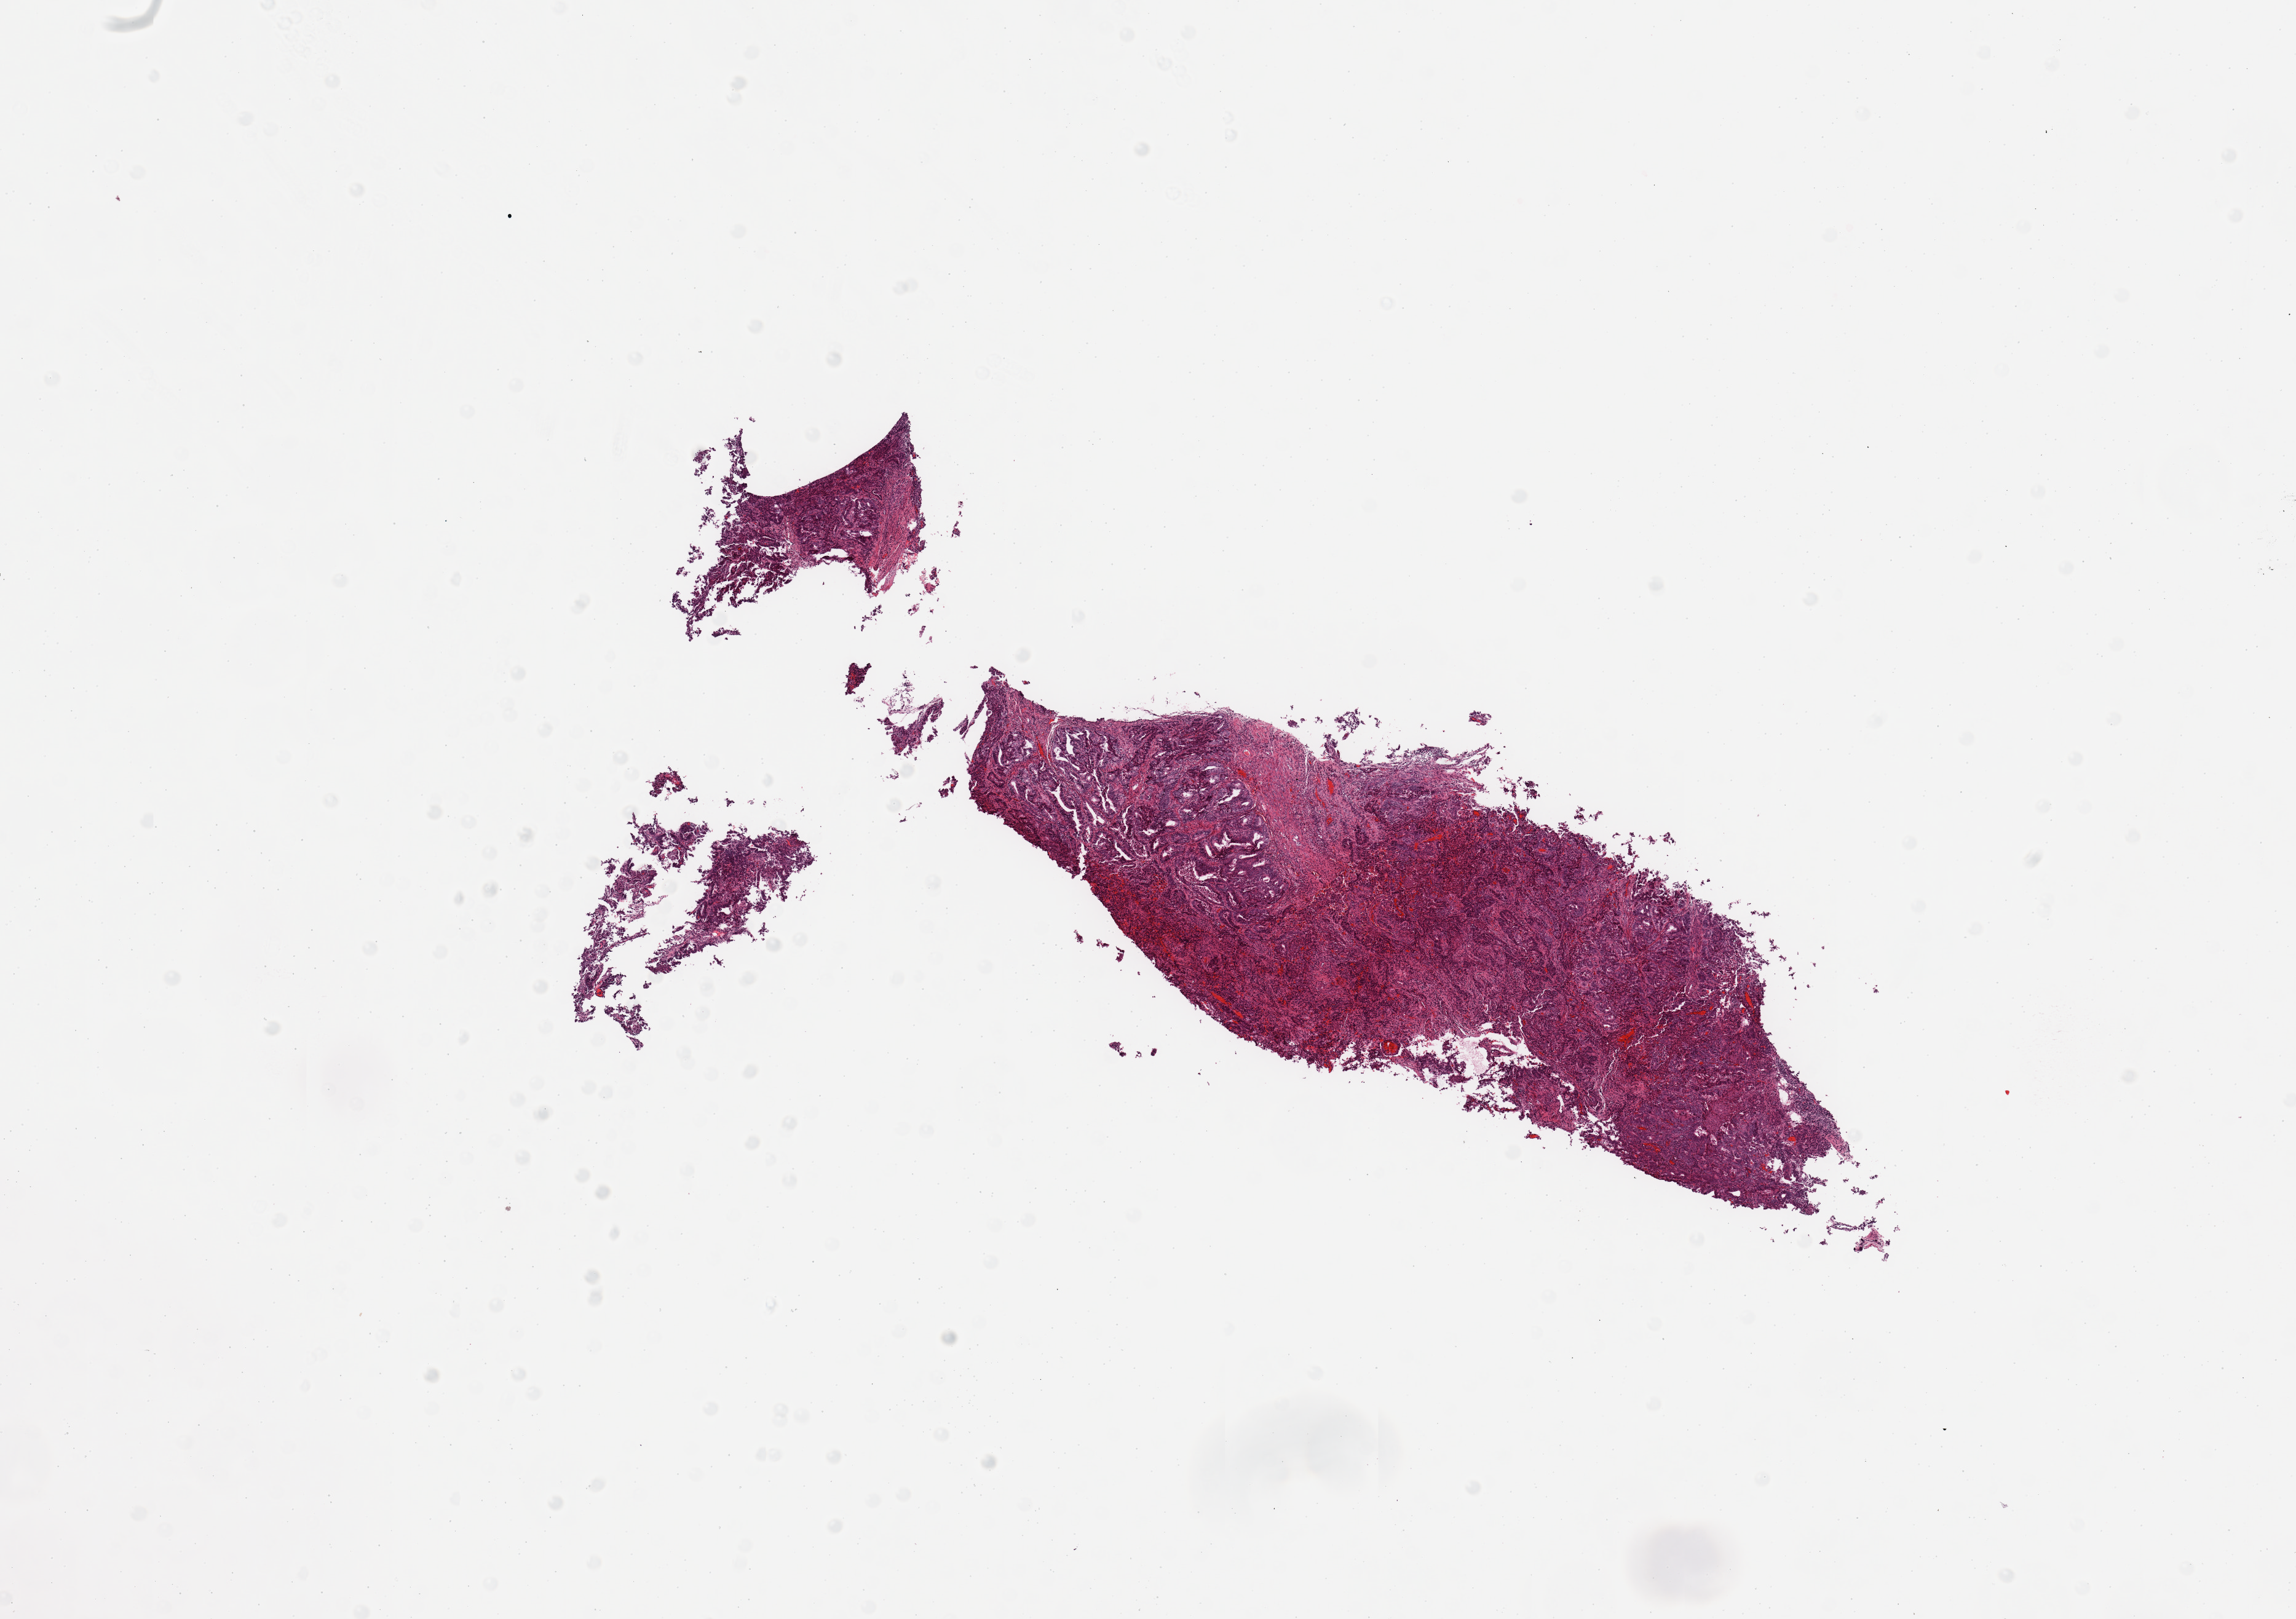
H&E whole-slide image — low-resolution overview of the scanned area, about 14.8 x 10.4 mm (slide scanned at 20x), tumour tissue sample, sampled site: uterus. 55-year-old female patient. Histologic grade: G1 (well differentiated). Pathologist review of this section (percent, as recorded): tumour nuclei 80%, necrosis 2%.
- primary tumour site (as recorded): anterior endometrium
- AJCC pathologic stage: I
- histologic diagnosis: Endometrioid adenocarcinoma, NOS